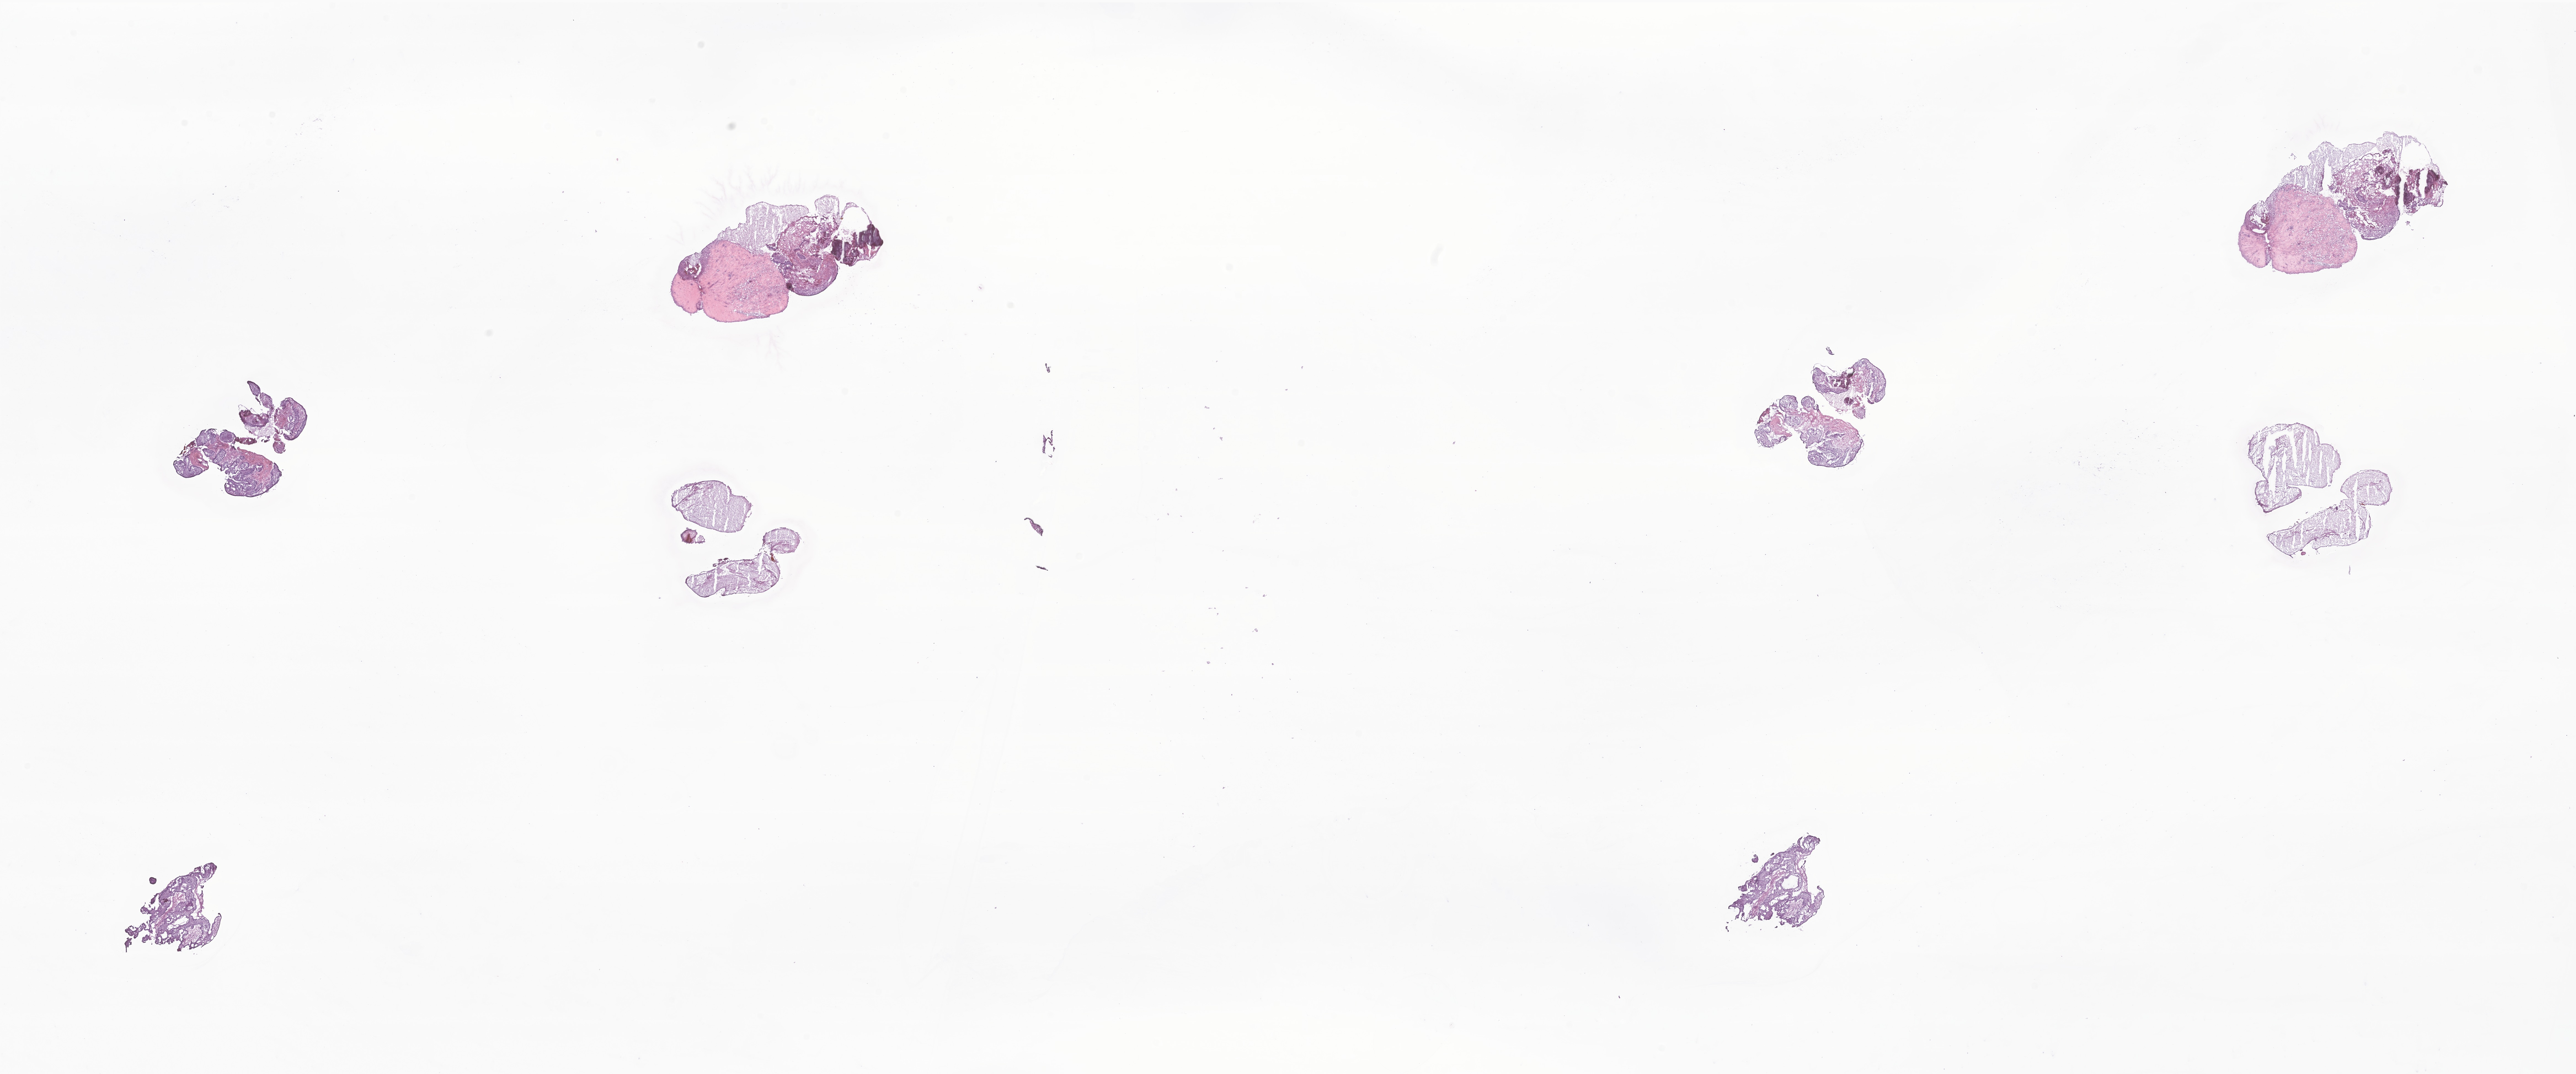
Digitized haematoxylin and eosin-stained section of tumor tissue from the brain — whole scanned area (about 39.4 x 16.4 mm) shown as a low-resolution overview. Frozen section (OCT-embedded). Patient male; age 173 months (14 years 5 months).
Recorded diagnosis: Neoplasm, uncertain whether benign or malignant.